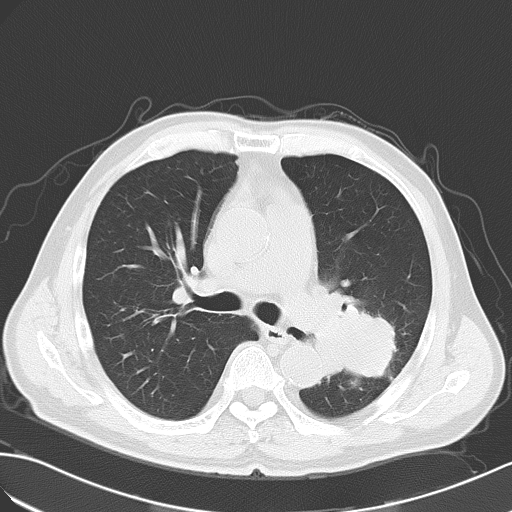
Chest CT, one axial slice; position 34 of 55 along the scan axis; reconstruction kernel B70f; lung window (W 1500 / L -600 HU); 5 mm slice thickness; 512 × 512 image matrix, field of view 353 × 353 mm. Male patient, age 63 years. From the clinical record (not read from this slice): clinical TNM (as recorded): T3 N3 M1a; histopathological grade: G3.
Structures marked on this image (rectangle marked by the reading radiologist):
- lung tumour (recorded histology: large cell carcinoma): bounding box <319,287,408,395> (left, top, right, bottom; pixels)